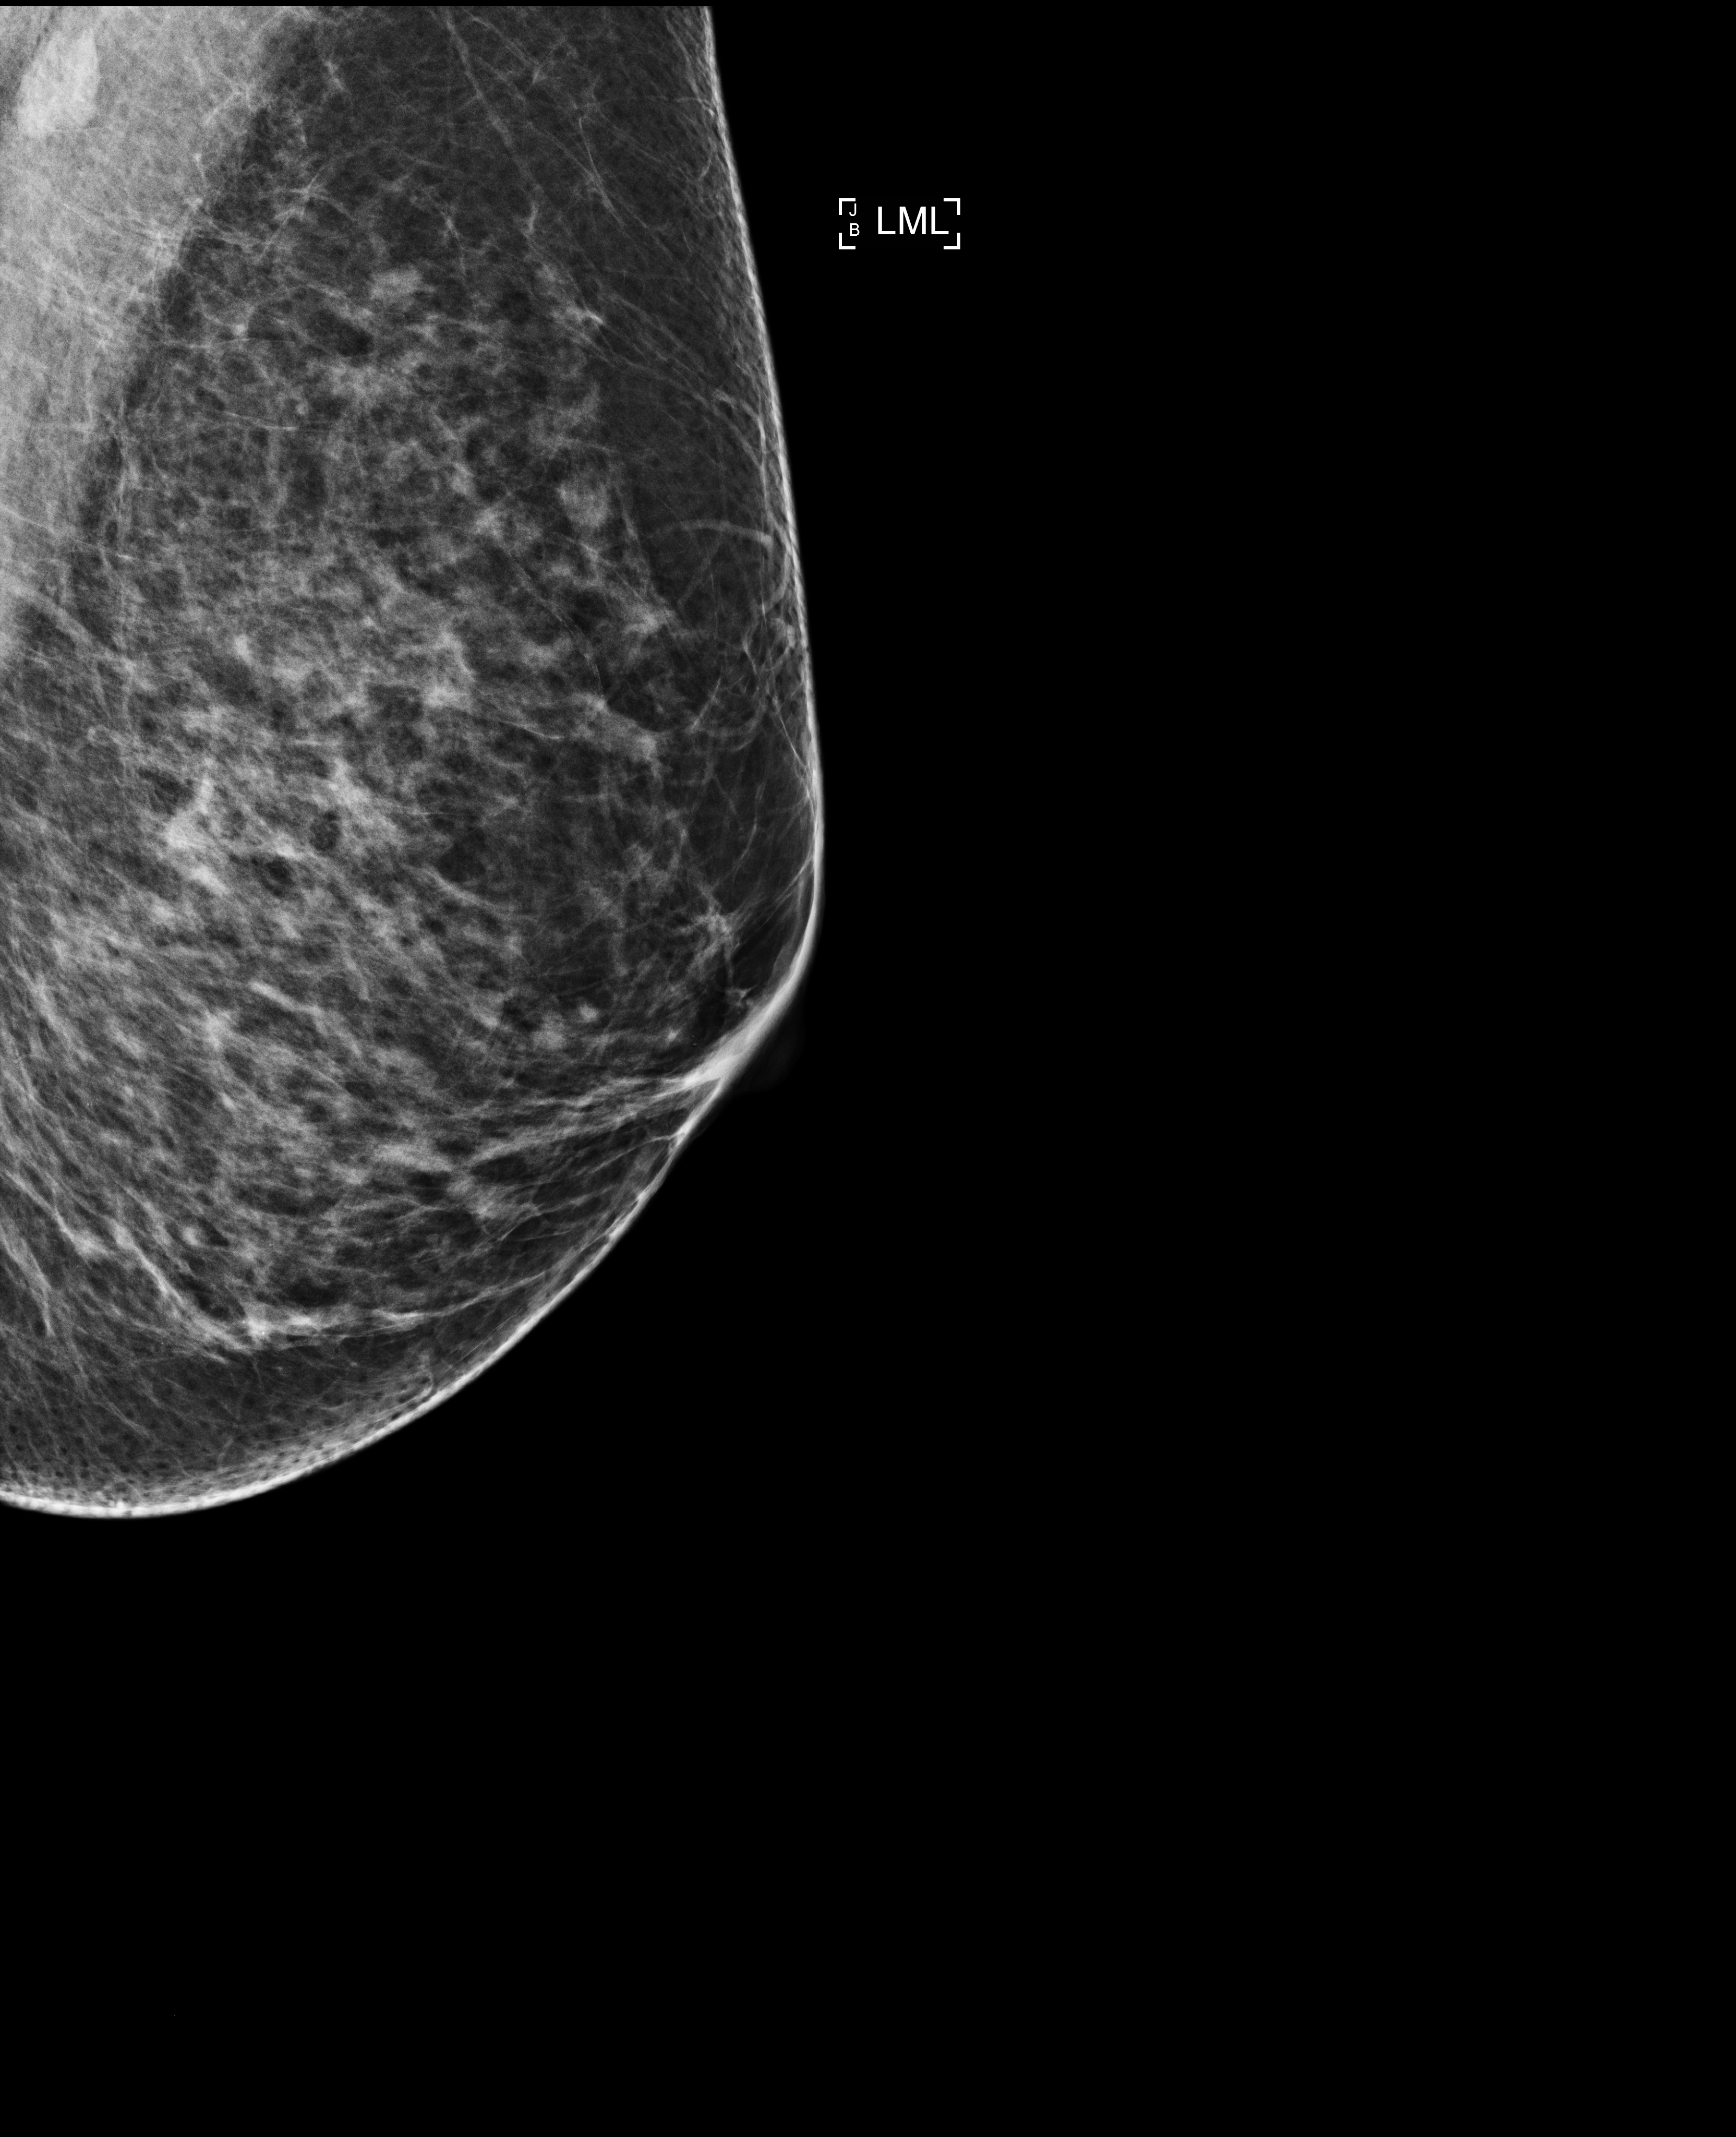
Full-field digital mammogram (FFDM), left breast, mediolateral (ML) view, diagnostic examination (additional views), compressed breast thickness 67 mm, system: Selenia Dimensions. Patient: female, 62 years.
Breast density at the screening exam (both breasts): scattered fibroglandular densities (BI-RADS density category b). Final BI-RADS assessment for this screening round (tomosynthesis exam, both breasts): category 2. Recall: recalled for additional imaging after this screen.